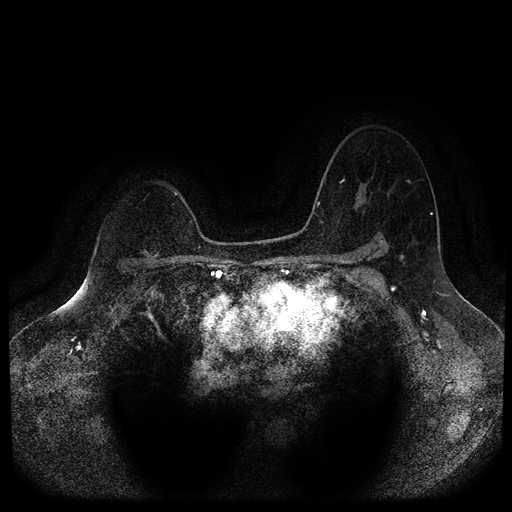
Breast MRI (dynamic contrast-enhanced, multi-phase), one axial slice. Slice 76 of 116 in the series (ordered by position). Dynamic contrast-enhanced series, time point 2 of 5 at this slice position (early post-contrast). 1.5 T. TE 2.6 ms, TR 5.4 ms. 512 × 512 image matrix. Patient: female, 64 years.
Outlined on this slice (semi-automatically segmented with operator editing):
- breast lesion (labelled benign in the annotation): bounding box [x1, y1, x2, y2] px = [144, 231, 162, 260]